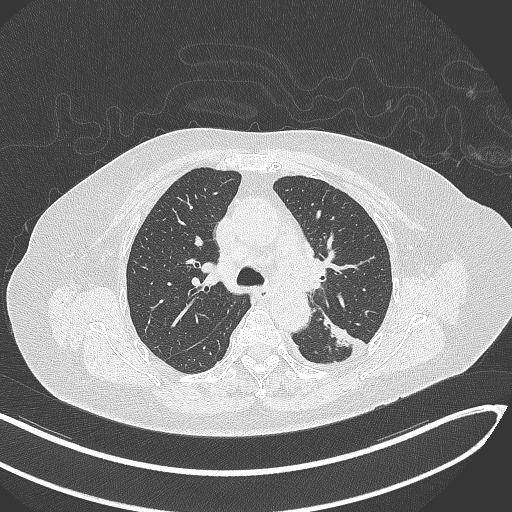
Chest CT, one axial slice; slice 212 of 270 in the series (ordered by position); 120 kVp; lung window (W 1500 / L -600 HU); 1 mm slice thickness; 512 × 512 image matrix, field of view 400 × 400 mm. Patient: female, 76 years. From the clinical record (not read from this slice): clinical TNM (as recorded): T1c N0 M0.
Annotated regions visible in this slice (rectangle marked by the reading radiologist):
- lung tumour (recorded histology: adenocarcinoma): bounding box (x1, y1, x2, y2) in pixels: (318, 309, 358, 356)